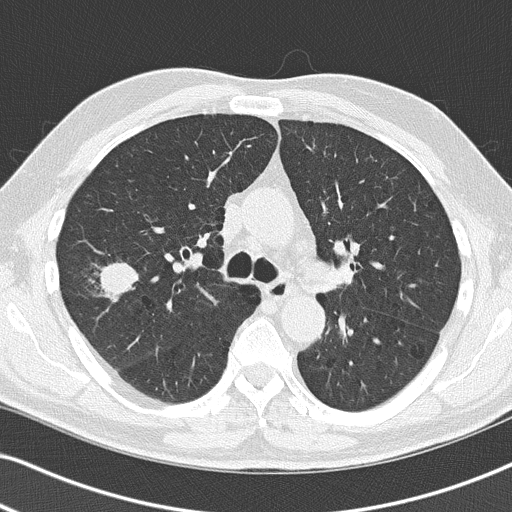
Chest CT (low-dose screening protocol), one axial image; baseline screening round; lung window (W 1500 / L -600 HU); lung (sharp) reconstruction kernel (B50f); 120 kVp. Male participant, aged 67 years at enrolment. Former smoker at enrolment.
Expert reader's lesion annotation, bounding box <73,254,149,316> (left, top, right, bottom; pixels). Reader record for this screening exam (exam-level; its link to the box is not recorded): non-calcified nodule or mass ≥4 mm, right upper lobe, 26 × 24 mm, spiculated (stellate) margins, soft tissue attenuation. Official screen result: positive, change unspecified: nodule(s) >= 4 mm or enlarging nodule(s), mass(es), or other non-specific abnormalities suspicious for lung cancer. Participant outcome: lung cancer diagnosed 49 days after this screen — squamous cell carcinoma, NOS, right upper lobe, poorly differentiated (G3), stage IA (AJCC 6th edition), 27 mm at pathology.